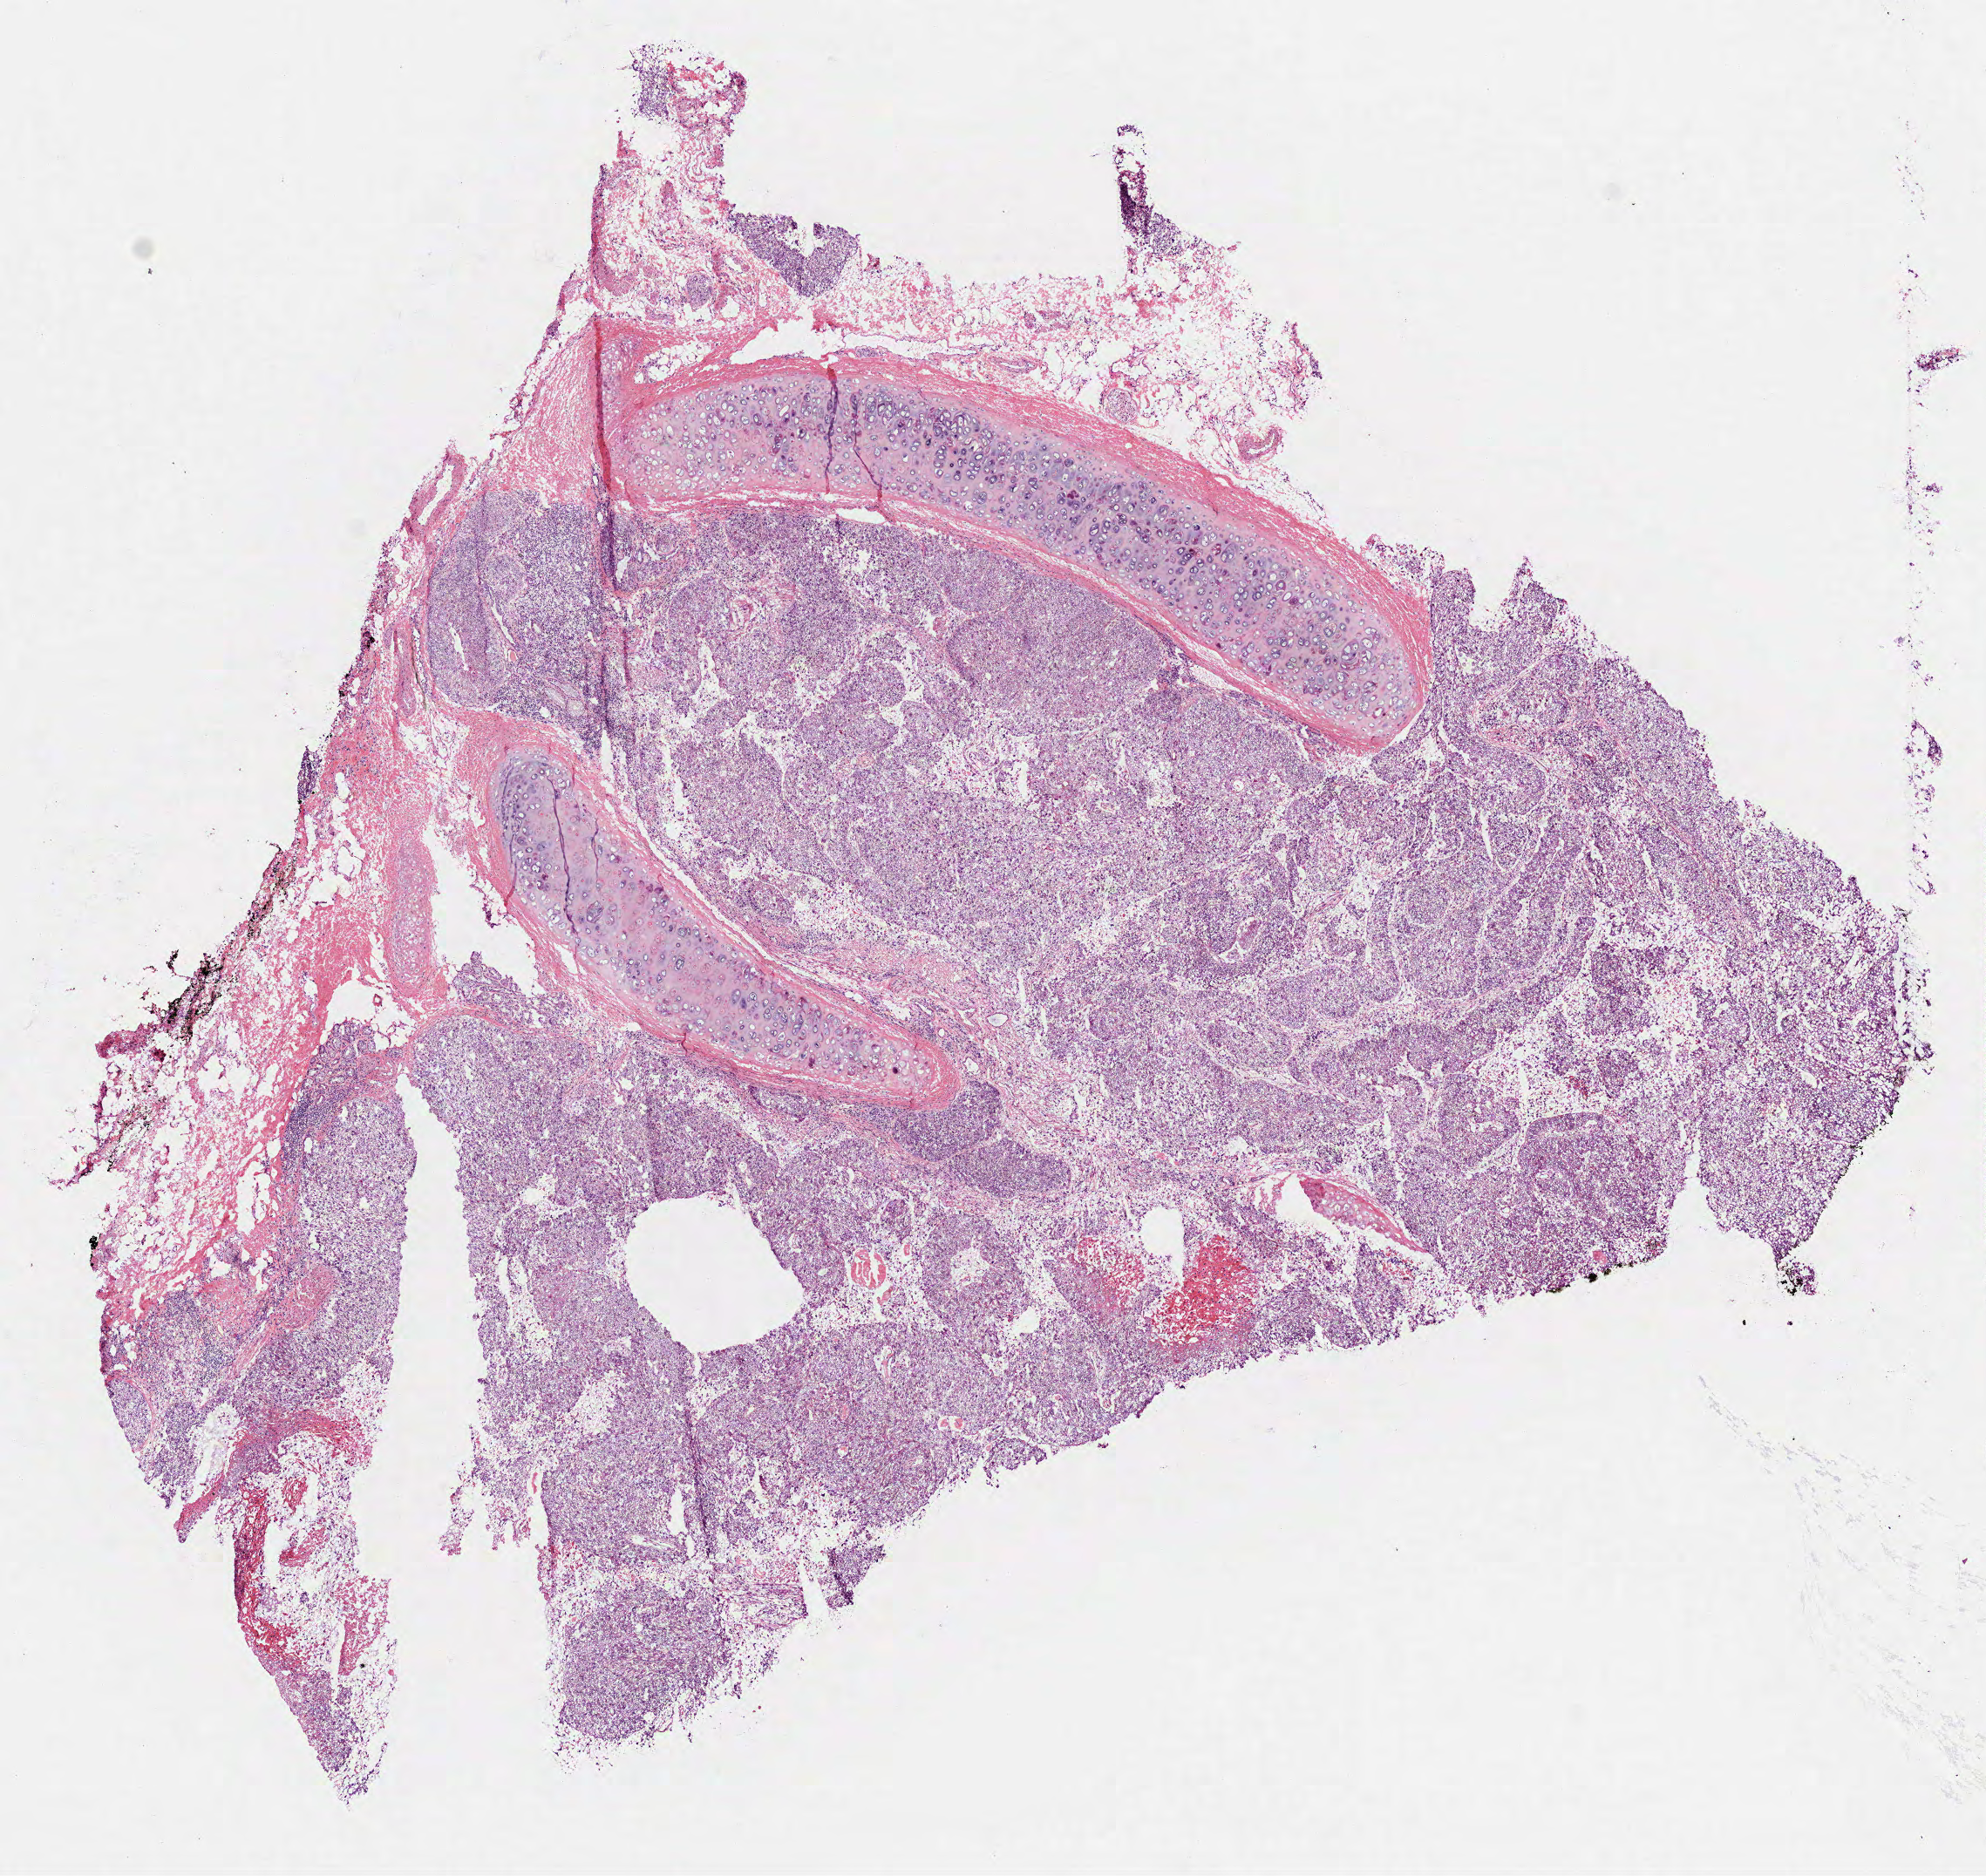
H&E whole-slide image, whole scanned area (about 9.2 x 8.7 mm, from a 40x scan) shown as a low-resolution overview, frozen section from the bottom of the tissue portion, sample: primary tumour, lung. Male patient; age at initial diagnosis 64 years. Slide review estimates, as recorded: tumour cells 72%, tumour nuclei 80%, normal cells 15%, stromal cells 10%, necrosis 3%.
Laterality: left. AJCC pathologic stage: IB (6th edition). Diagnosis: Squamous cell carcinoma, NOS (upper lobe, lung).